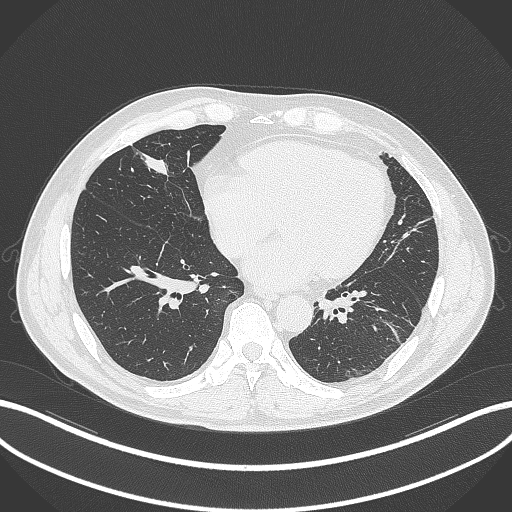
Chest CT, one axial slice. Slice 97 of 399 in the series (ordered by position). Reconstruction kernel B70f. Lung window (W 1500 / L -600 HU). 1 mm slice thickness. 512 × 512 image matrix, field of view 400 × 400 mm. Patient: male, 59 years. Case-level facts recorded for this patient, not image findings: clinical TNM (as recorded): T2a N1 M0.
Annotated regions visible in this slice (bounding box drawn by a radiologist):
- lung tumour (recorded histology: adenocarcinoma): bounding box (x1, y1, x2, y2) in pixels: (131, 144, 179, 181)